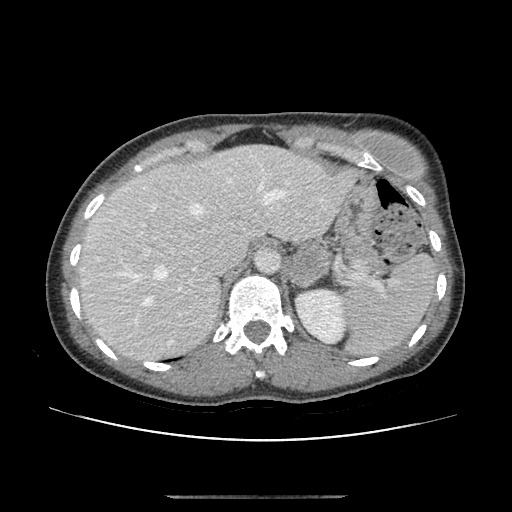
Contrast-enhanced abdominal CT, one axial slice. Position 78 of 179 along the scan axis. Soft-tissue window (W 400 / L 40 HU). 2.5 mm slice thickness. 512 × 512 image matrix, field of view 360 × 360 mm. Patient: female, 51 years. Case-level facts recorded for this patient, not image findings: diagnosis: adrenocortical carcinoma; tumour side: left adrenal; tumour size at pathology: 3.5 cm; Ki-67 index: 45 %; stage (as recorded): 1.
Annotated regions visible in this slice (semi-automatic segmentation, software-assisted and operator-edited):
- mass: bounding box [x1, y1, x2, y2] px = [291, 242, 327, 285]